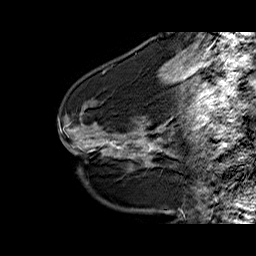
Breast MRI (dynamic contrast-enhanced), one sagittal slice. Slice 19 of 60 in the series (ordered by position). Dynamic contrast-enhanced series, time point 2 of 6 at this slice position (early post-contrast). 1.5 T. TE 6.3 ms, TR 32.5 ms. 4 mm slice thickness. 256 × 256 image matrix, field of view 200 × 200 mm. Female patient. Case-level facts recorded for this patient, not image findings: setting: breast cancer imaged before/during neoadjuvant chemotherapy; receptor status: HR-positive, HER2-negative.
Structures marked on this image (semi-automatic segmentation, software-assisted and operator-edited):
- analysis volume of interest (the breast-tissue region the enhancement analysis was run in; not a lesion): bounding box <94,121,161,164> (left, top, right, bottom; pixels)
- tumour enhancement mask (voxels above the 100 % enhancement threshold inside the analysis volume of interest): <149,147,152,151>